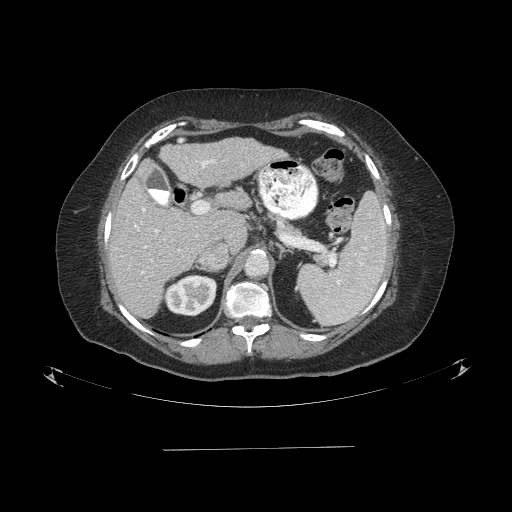
Contrast-enhanced abdominal CT (liver protocol), one axial slice; position 51 of 103 along the scan axis; reconstruction kernel STANDARD; one of 2 acquisitions stored at this slice position; soft-tissue window (W 400 / L 40 HU); 2.5 mm slice thickness; 512 × 512 image matrix. From the clinical record (not read from this slice): diagnosis: hepatocellular carcinoma (patient treated with transarterial chemoembolisation; whether this scan precedes or follows treatment is not stated here); TNM stage (as recorded): Stage-IIIA; Child-Pugh class: A; tumour differentiation: poorly differentiated.
Annotated regions visible in this slice (semi-automatically segmented with operator editing):
- liver parenchyma outside the tumour (the mass and vessels are separate outlines, so this box may not span the whole liver): box from (x=108, y=138) to (x=284, y=318) px
- liver vessels: (x=134, y=160)–(x=214, y=274)